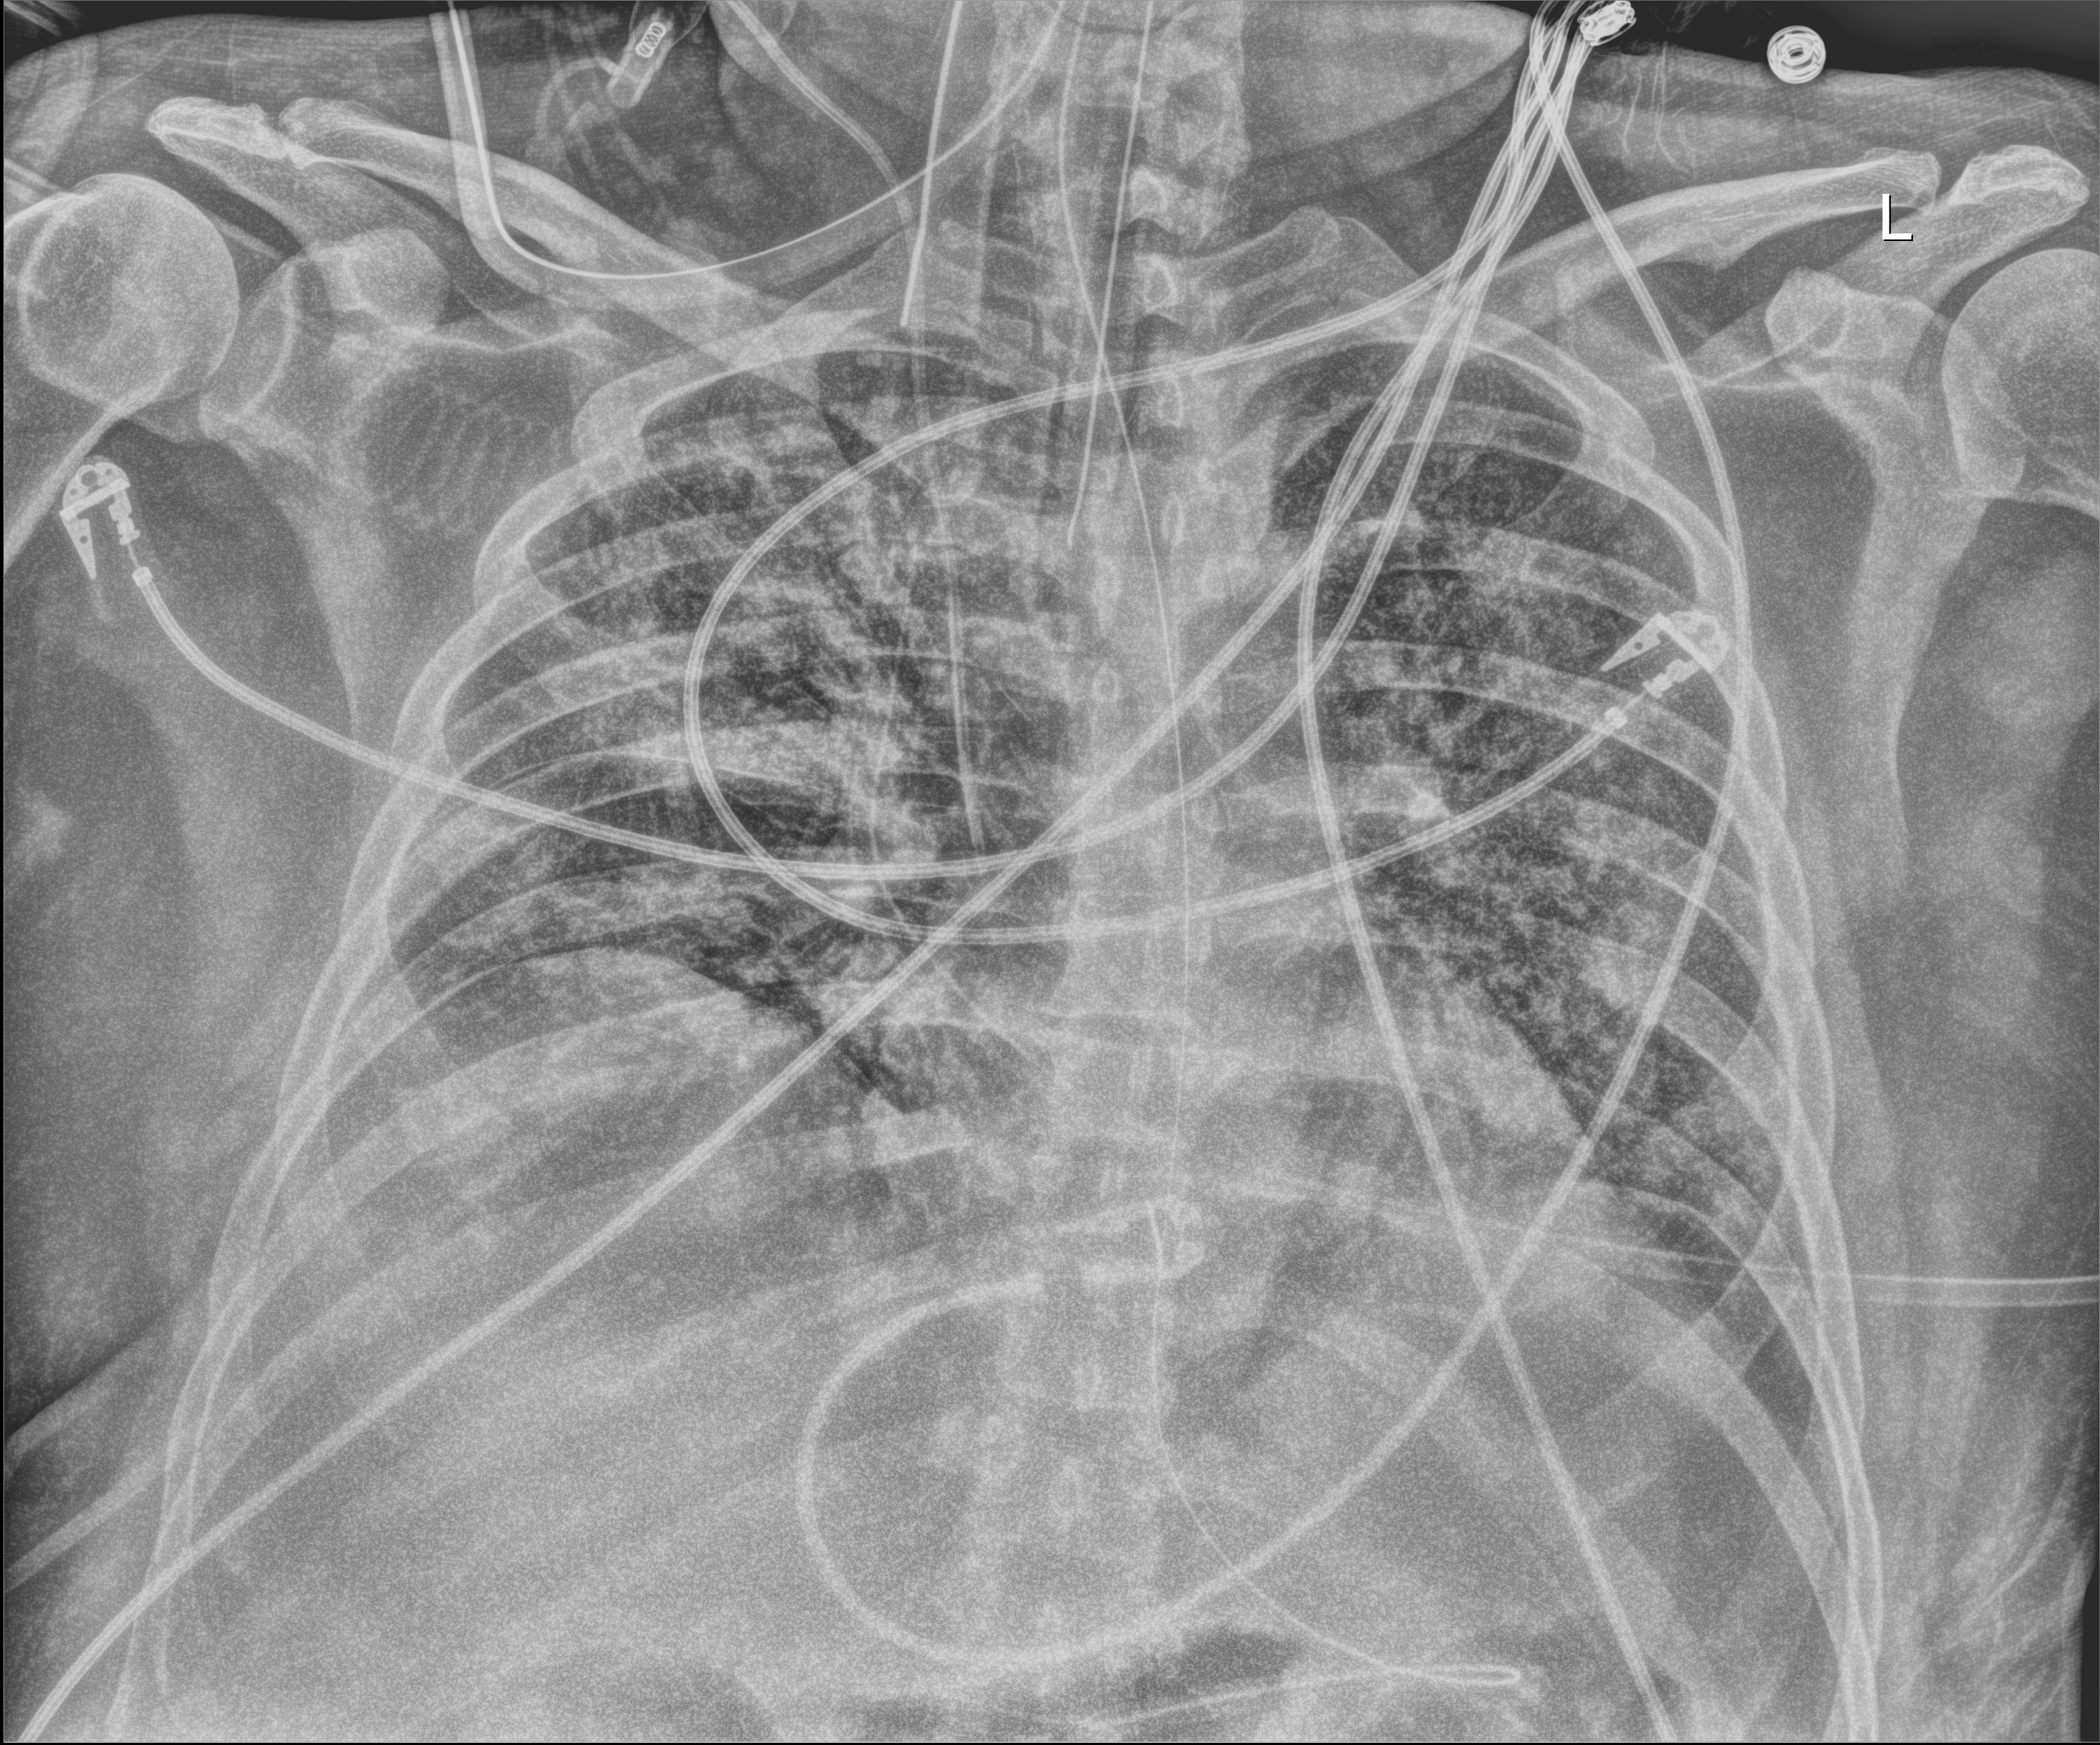
Bedside chest radiograph (digital radiography). Male patient hospitalised with COVID-19, age 18–59 years.
Hospital-stay facts (about this admission, not read from this image; timing relative to this image not recorded): other chronic lung disease (admission record): no; smoking status (admission record): never; COPD (admission record): no.